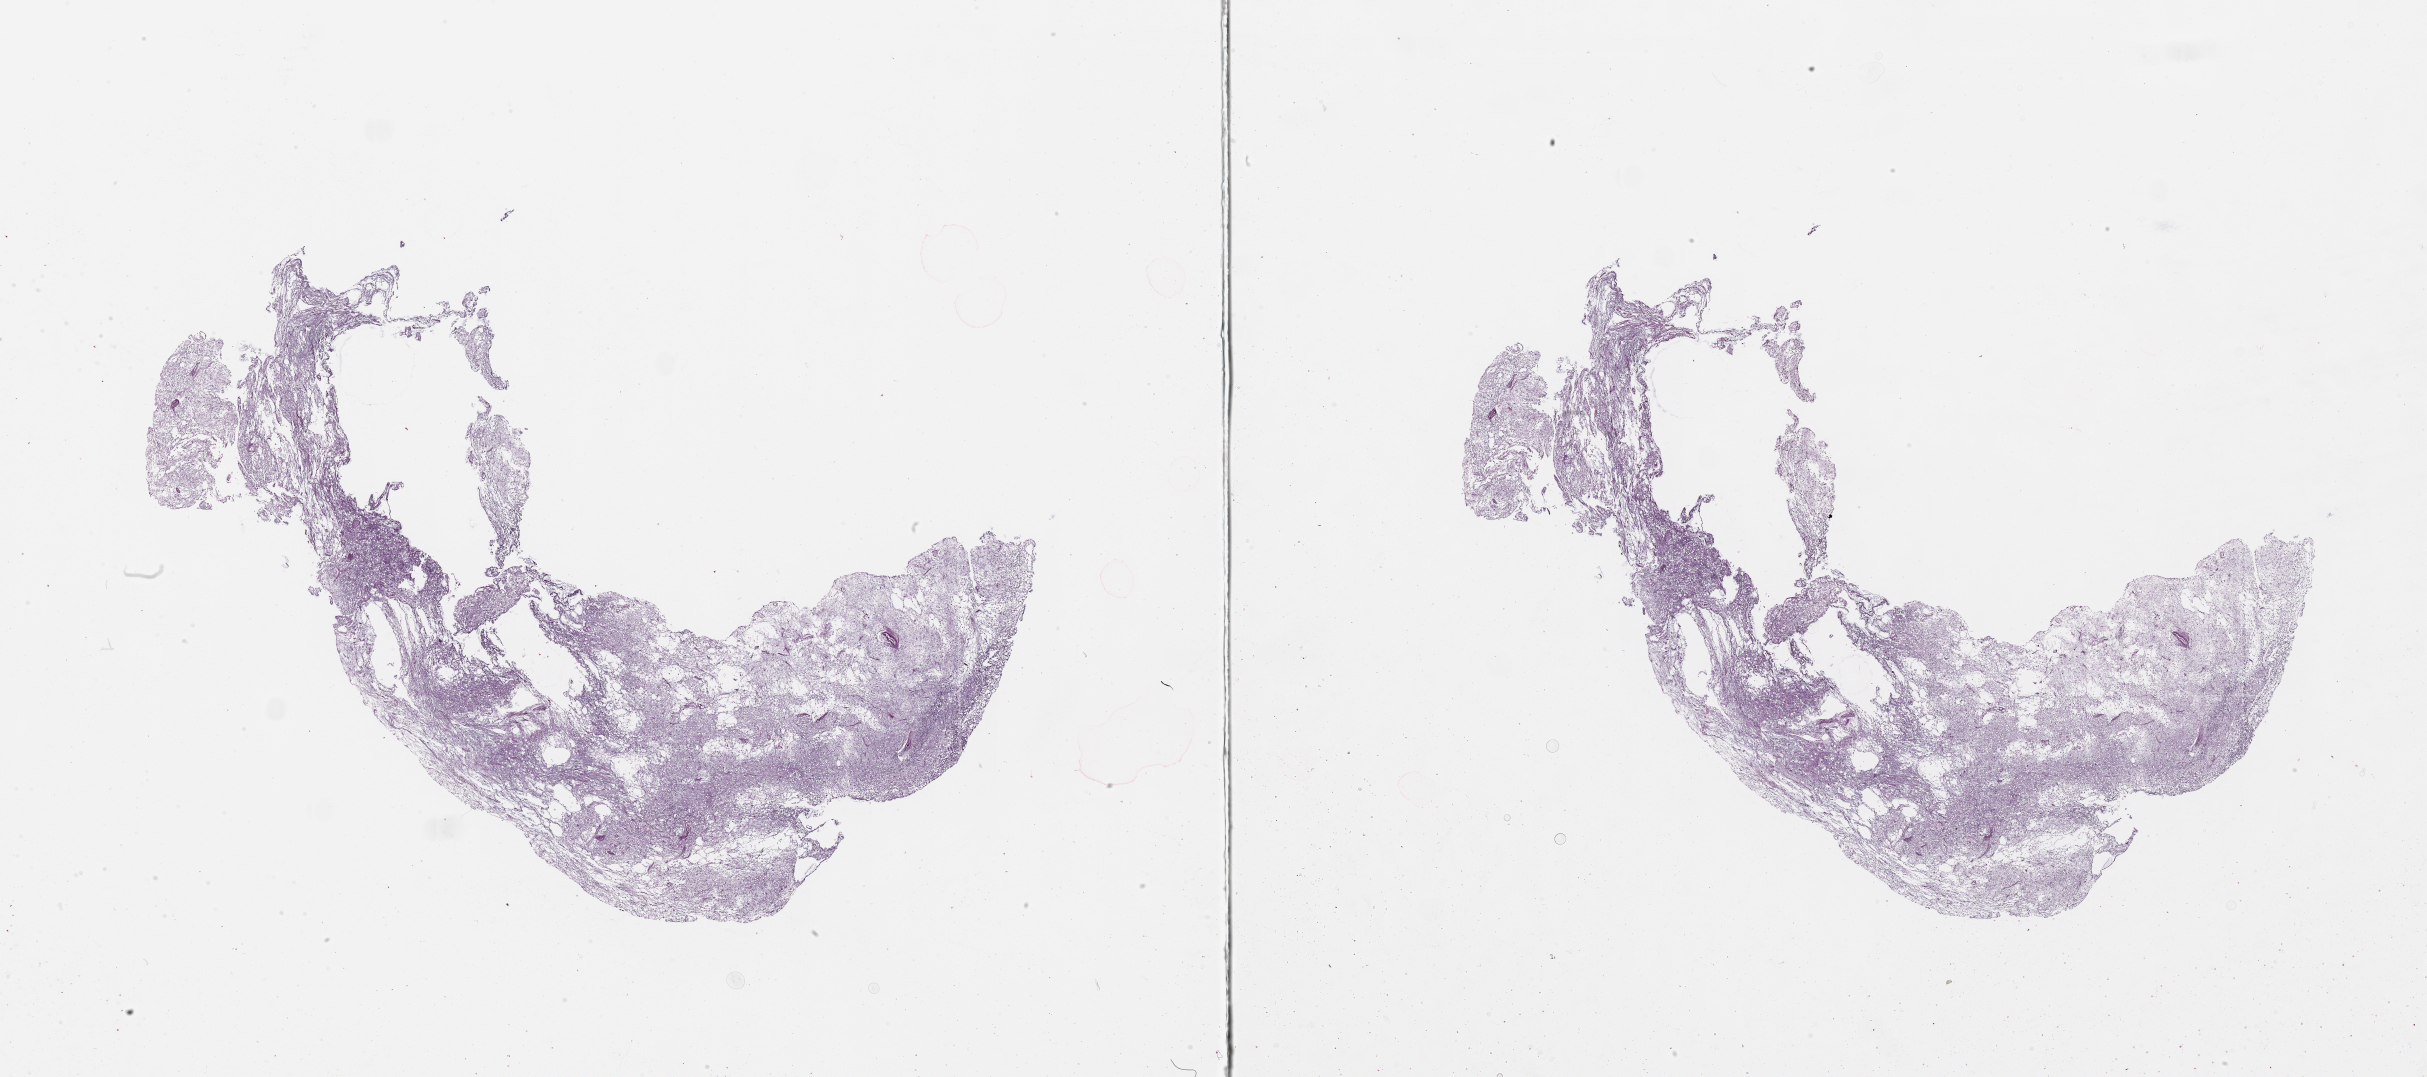
Digitized H&E-stained tissue section (whole slide) — low-resolution overview of the scanned area, about 39.1 x 17.3 mm (from a 20x scan); tumour tissue sample. 78-year-old female patient.
* patient diagnosis (cohort enrolment): sarcoma (site not recorded at cohort level)
* primary tumour site (as recorded): lower extremity